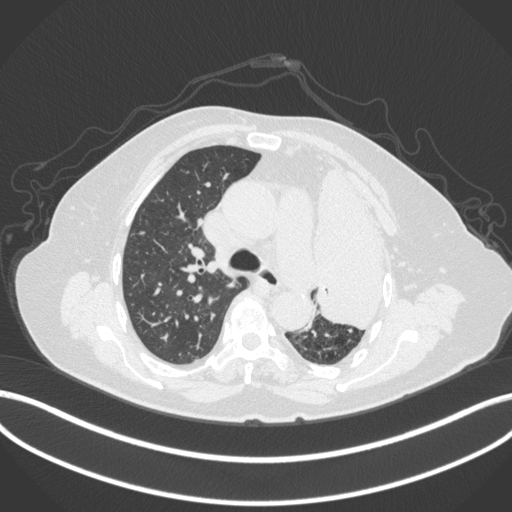
Chest CT, one axial slice; slice 263 of 399 in the series (ordered by position); reconstruction kernel B31f; 120 kVp; lung window (W 1500 / L -600 HU); 512 × 512 image matrix, field of view 400 × 400 mm. Patient: female, 75 years. From the clinical record (not read from this slice): clinical TNM (as recorded): T3 N3 M1.
Annotated regions visible in this slice (rectangle marked by the reading radiologist):
- lung tumour (recorded histology: adenocarcinoma): bounding box [x1, y1, x2, y2] px = [310, 156, 406, 333]